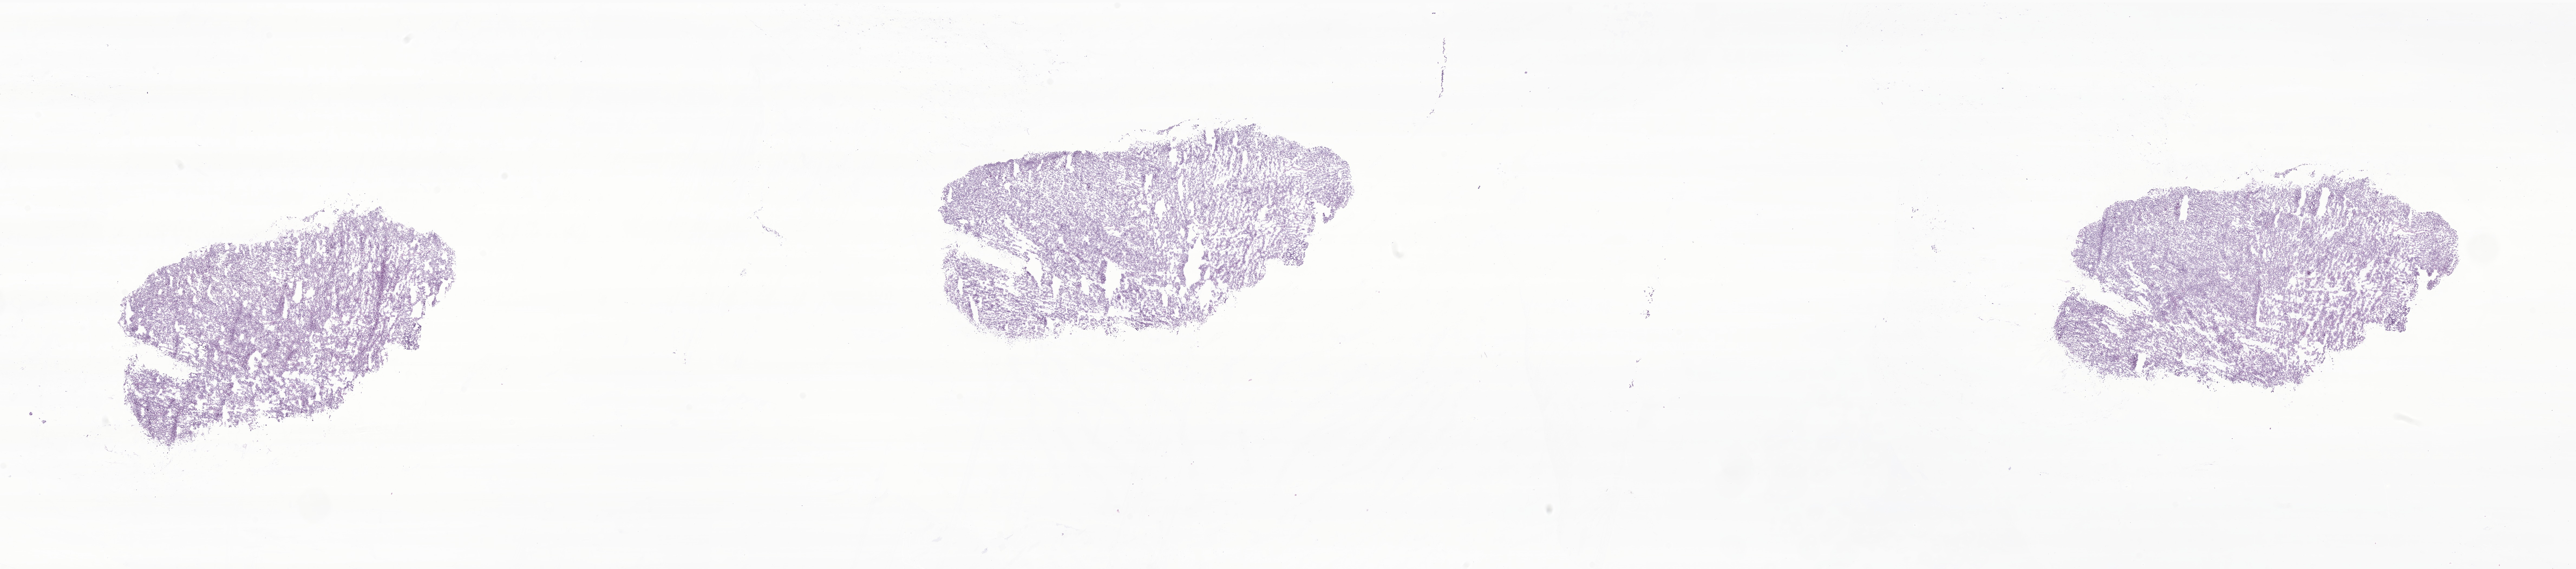
Whole-slide image, haematoxylin and eosin stain of tumor tissue from the central nervous system — a low-resolution overview of the entire scanned area, about 40.1 x 8.9 mm; cryosection (OCT / tissue freezing medium). Patient: female, age 184 months (15 years 4 months).
Recorded diagnosis: Glioblastoma, NOS.